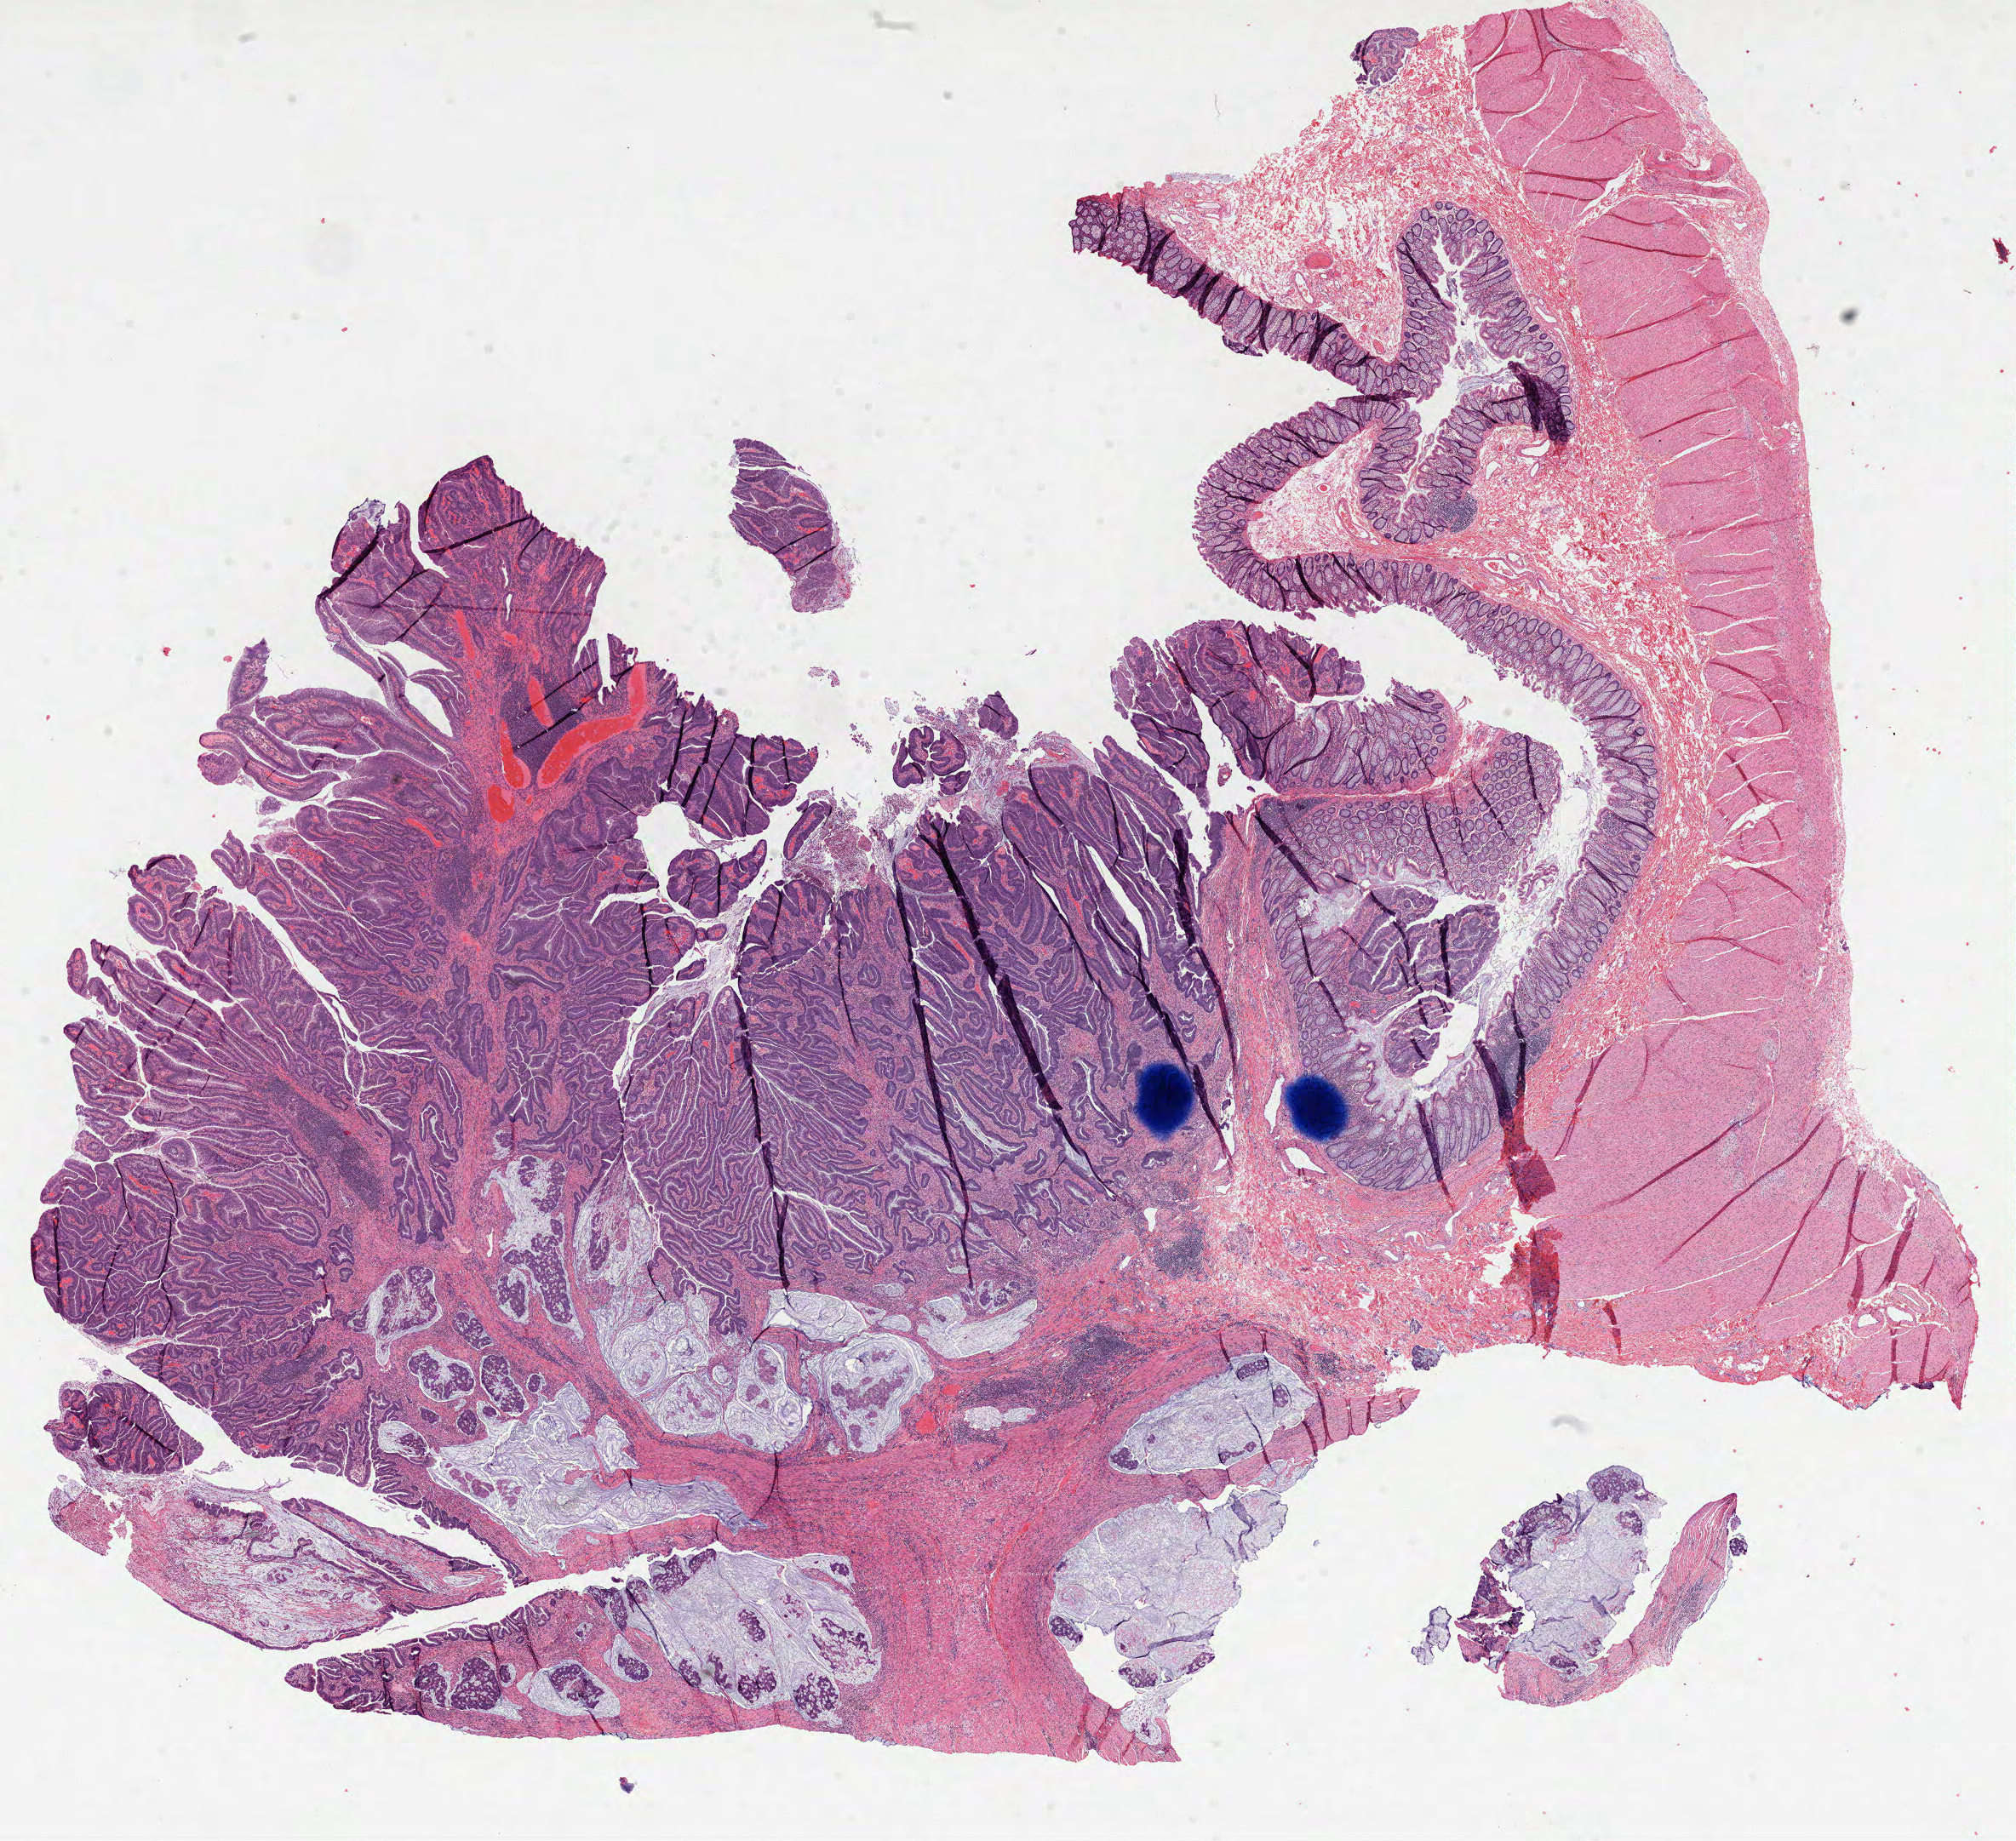
Digitized H&E tissue section (whole slide) — a low-resolution overview of the entire scanned area, about 19.1 x 17.4 mm, formalin-fixed paraffin-embedded (FFPE) diagnostic section, primary tumour sample from the colon. Female patient; age at initial diagnosis 48 years.
Pathologic diagnosis: Mucinous adenocarcinoma (ascending colon).